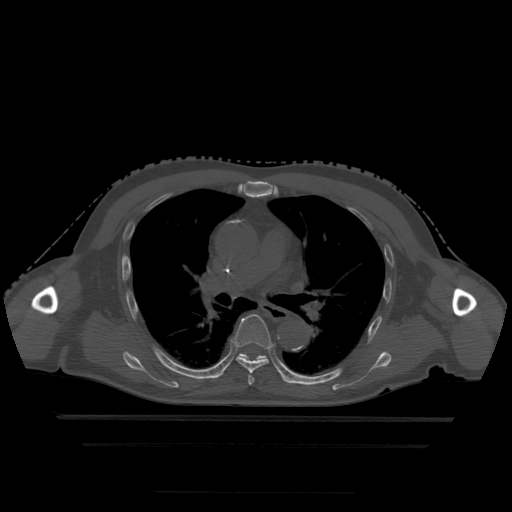
CT including the spine, one axial slice; position 315 of 522 along the scan axis; bone window (W 1800 / L 400 HU); 512 × 512 image matrix, field of view 436 × 436 mm. Patient age 68 years. From the clinical record (not read from this slice): primary cancer: urothelial.
Outlined on this slice (semi-automatically segmented with operator editing):
- T5 vertebra: bounding box <248,376,255,385> (left, top, right, bottom; pixels)
- T6 vertebra: <233,314,273,374>
- T7 vertebra: <239,354,267,361>